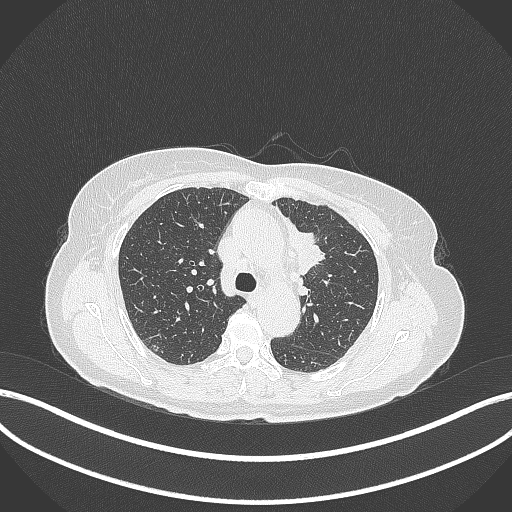
Chest CT, one axial slice. Slice 233 of 369 in the series (ordered by position). Reconstruction kernel B70f. Lung window (W 1500 / L -600 HU). 1 mm slice thickness. 512 × 512 image matrix, field of view 400 × 400 mm. Patient: female, 65 years. From the clinical record (not read from this slice): clinical TNM (as recorded): T2a N0 M0; histopathological grade: G2-3.
Outlined on this slice (bounding box drawn by a radiologist):
- lung tumour (recorded histology: adenocarcinoma): bounding box [x1, y1, x2, y2] px = [282, 214, 327, 277]